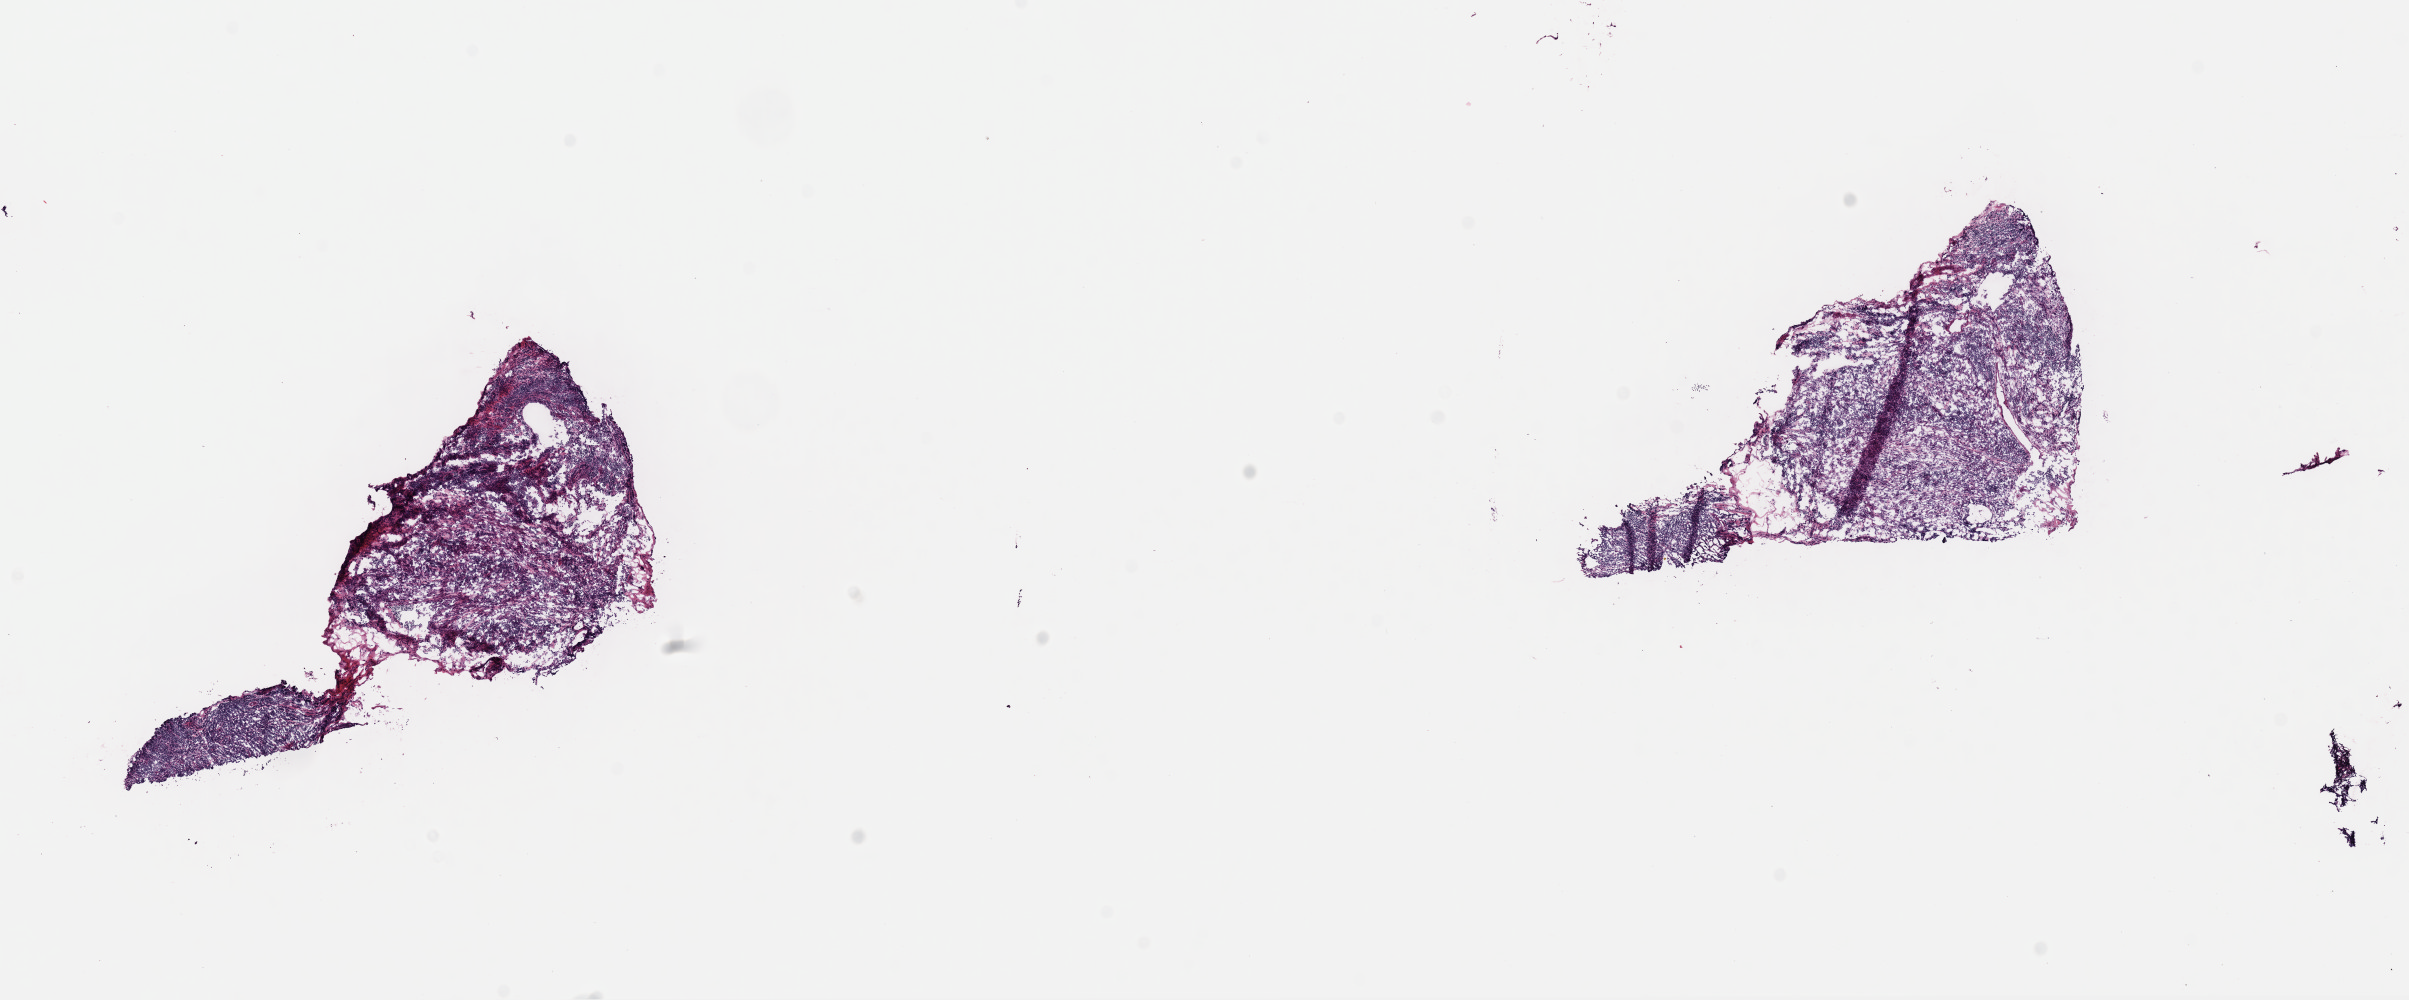
Whole-slide histology image, H&E, shown as a low-resolution overview of the whole scanned area (about 19.0 x 7.9 mm, from a 40x scan). Frozen section from the top of the tissue portion. Metastatic tumour sample, sampled site: lymph nodes of axilla or arm. Male patient; age at initial diagnosis 61 years. Slide review estimates, as recorded: tumour cells 75%, tumour nuclei 75%, normal cells 0%, stromal cells 25%, necrosis 0%. Inflammatory infiltration, as recorded: lymphocyte infiltration 5%, monocyte infiltration 1%, neutrophil infiltration 0%.
This section: metastatic tumour tissue. Patient diagnosis: Malignant melanoma, NOS.